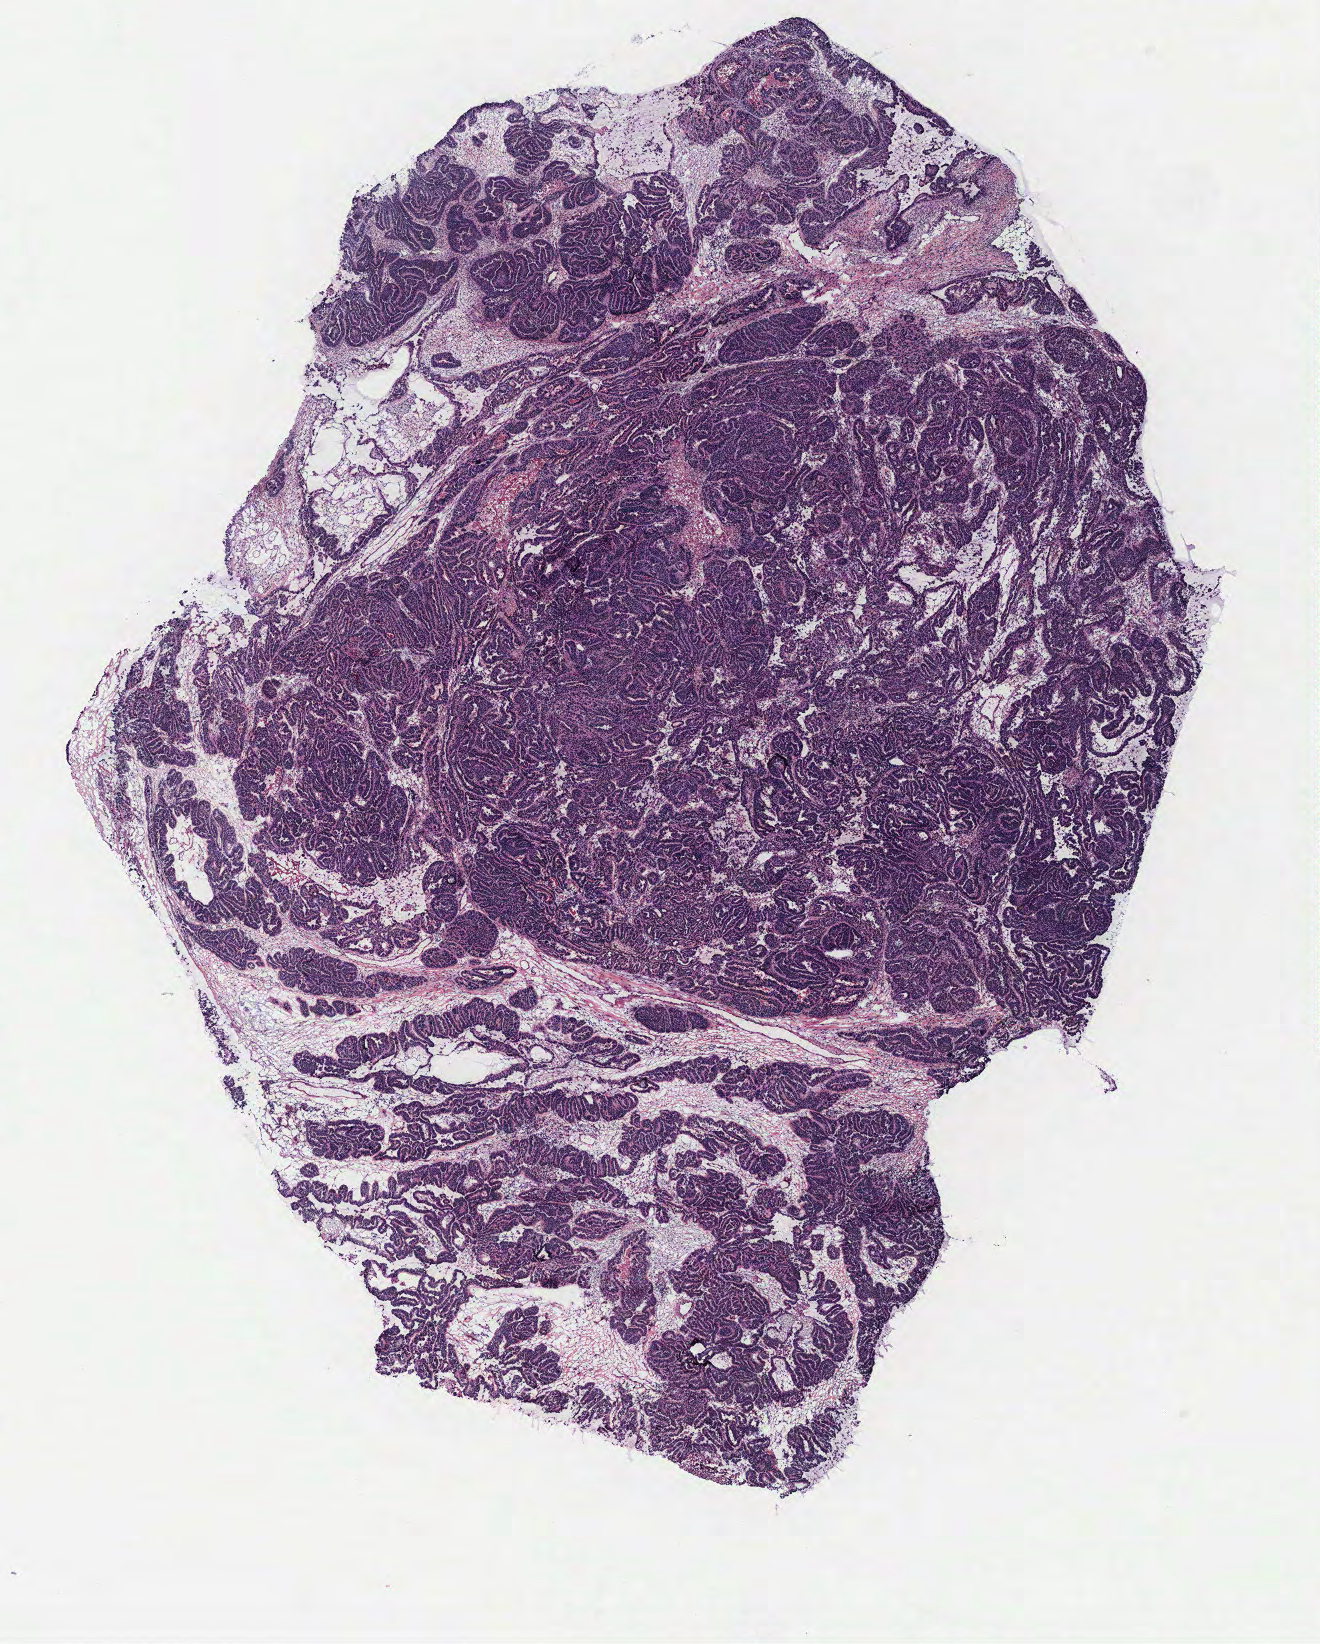
Whole-slide histology image, H&E-stained, whole scanned area (about 10.6 x 13.2 mm) shown as a low-resolution overview; ovary, tissue type not recorded. Patient sex: female.
Patient diagnosis: Serous adenocarcinoma, NOS.